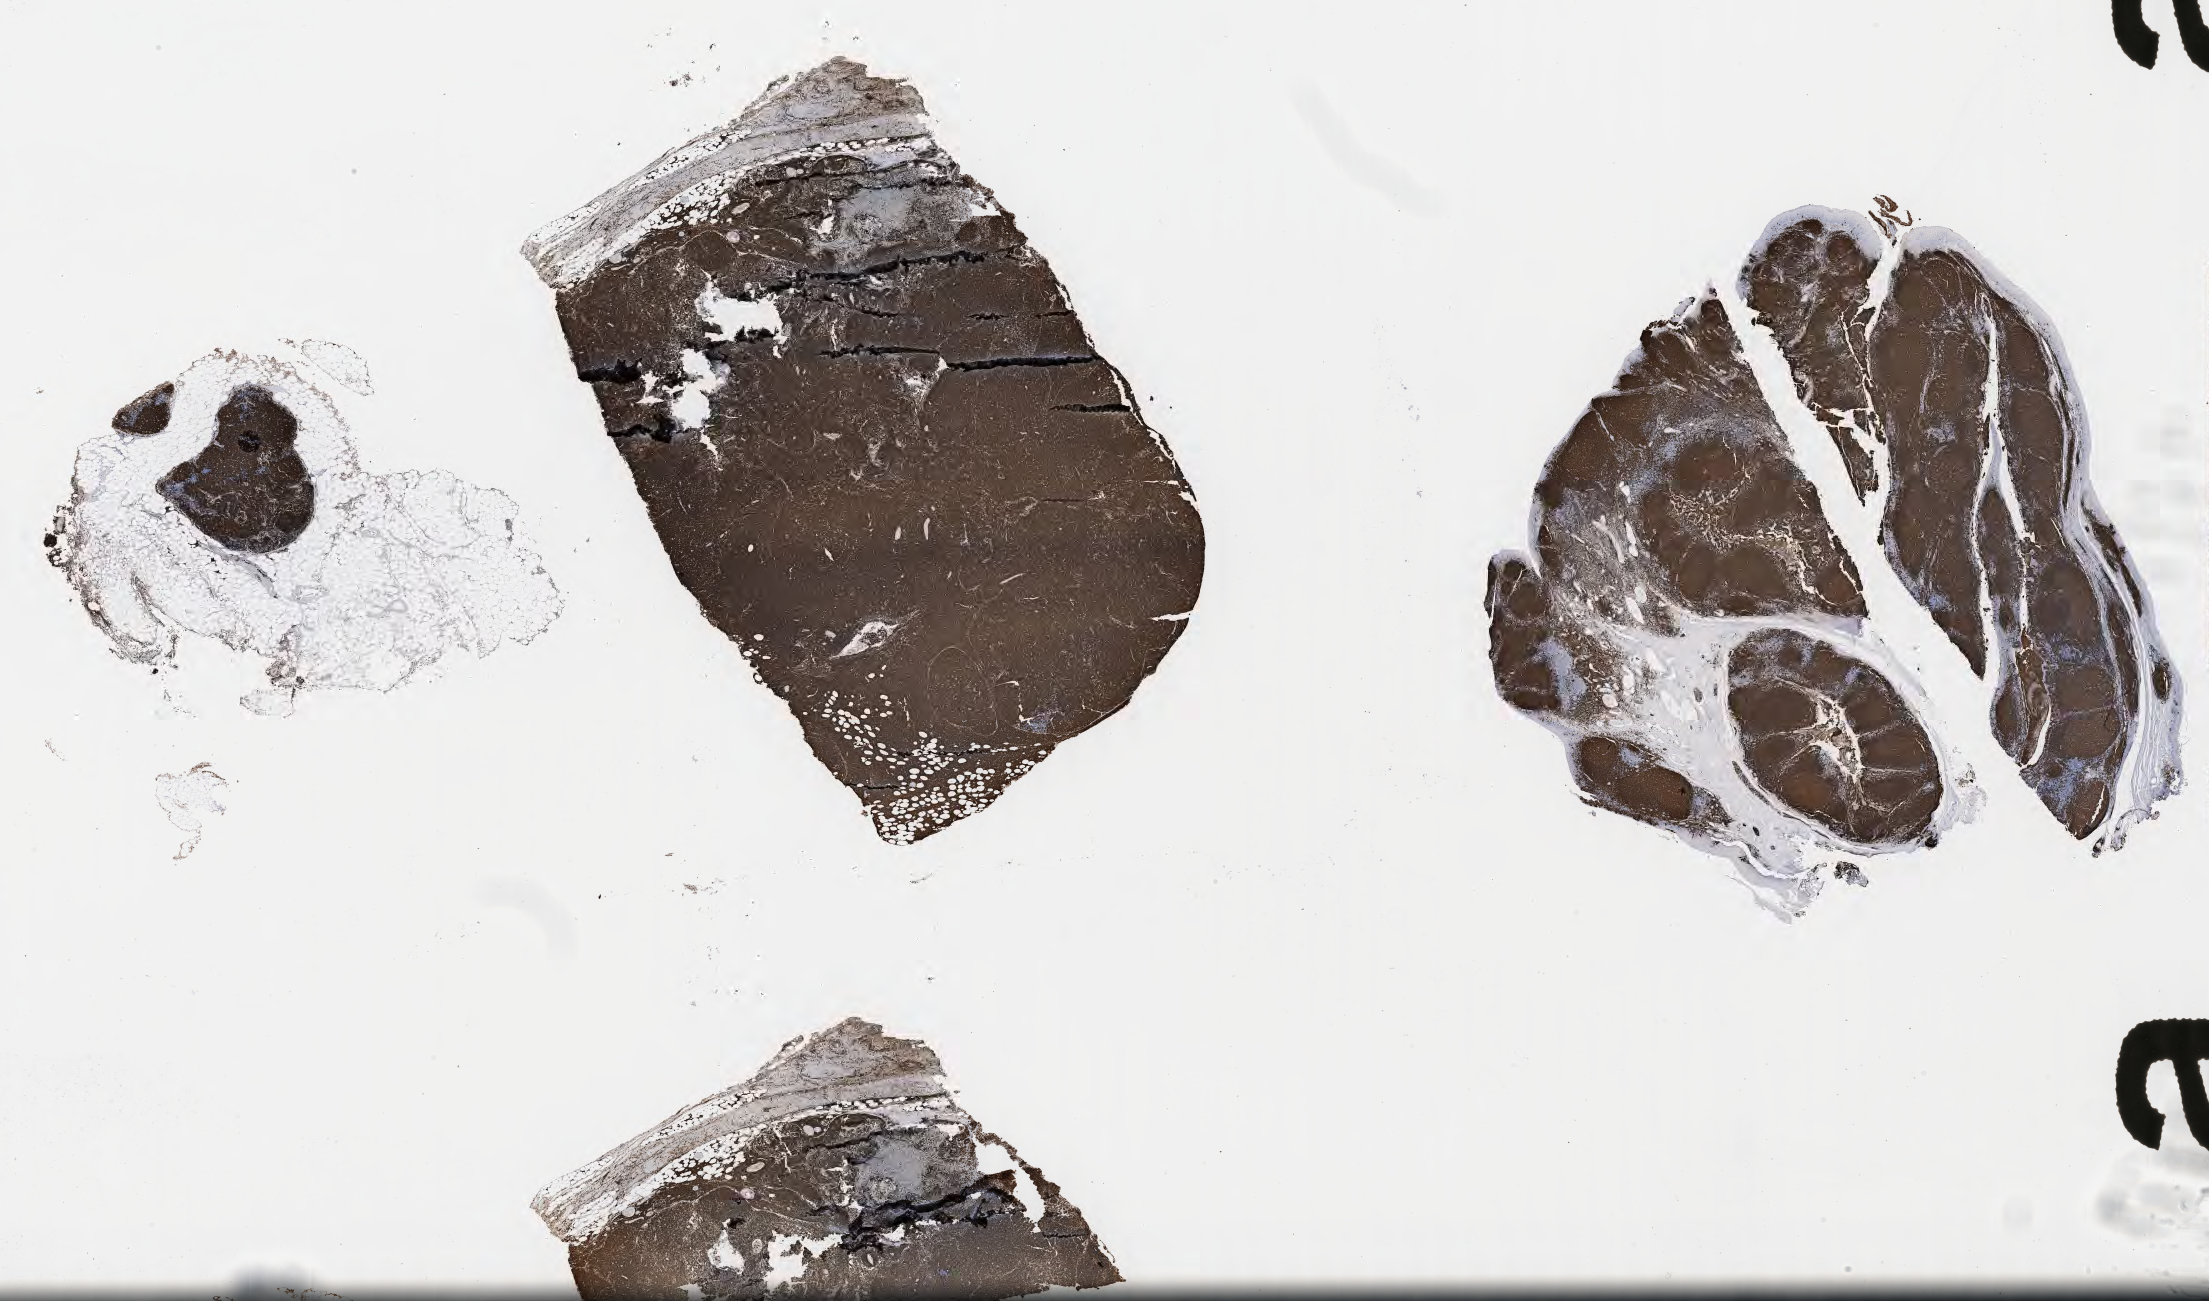
Immunohistochemistry (IHC) whole-slide image stained for CD20, shown as a low-resolution overview of the whole scanned area (about 35.7 x 21.0 mm); specimen: tumor tissue. Patient: male, 40 years old.
- histologic diagnosis: Burkitt lymphoma, NOS